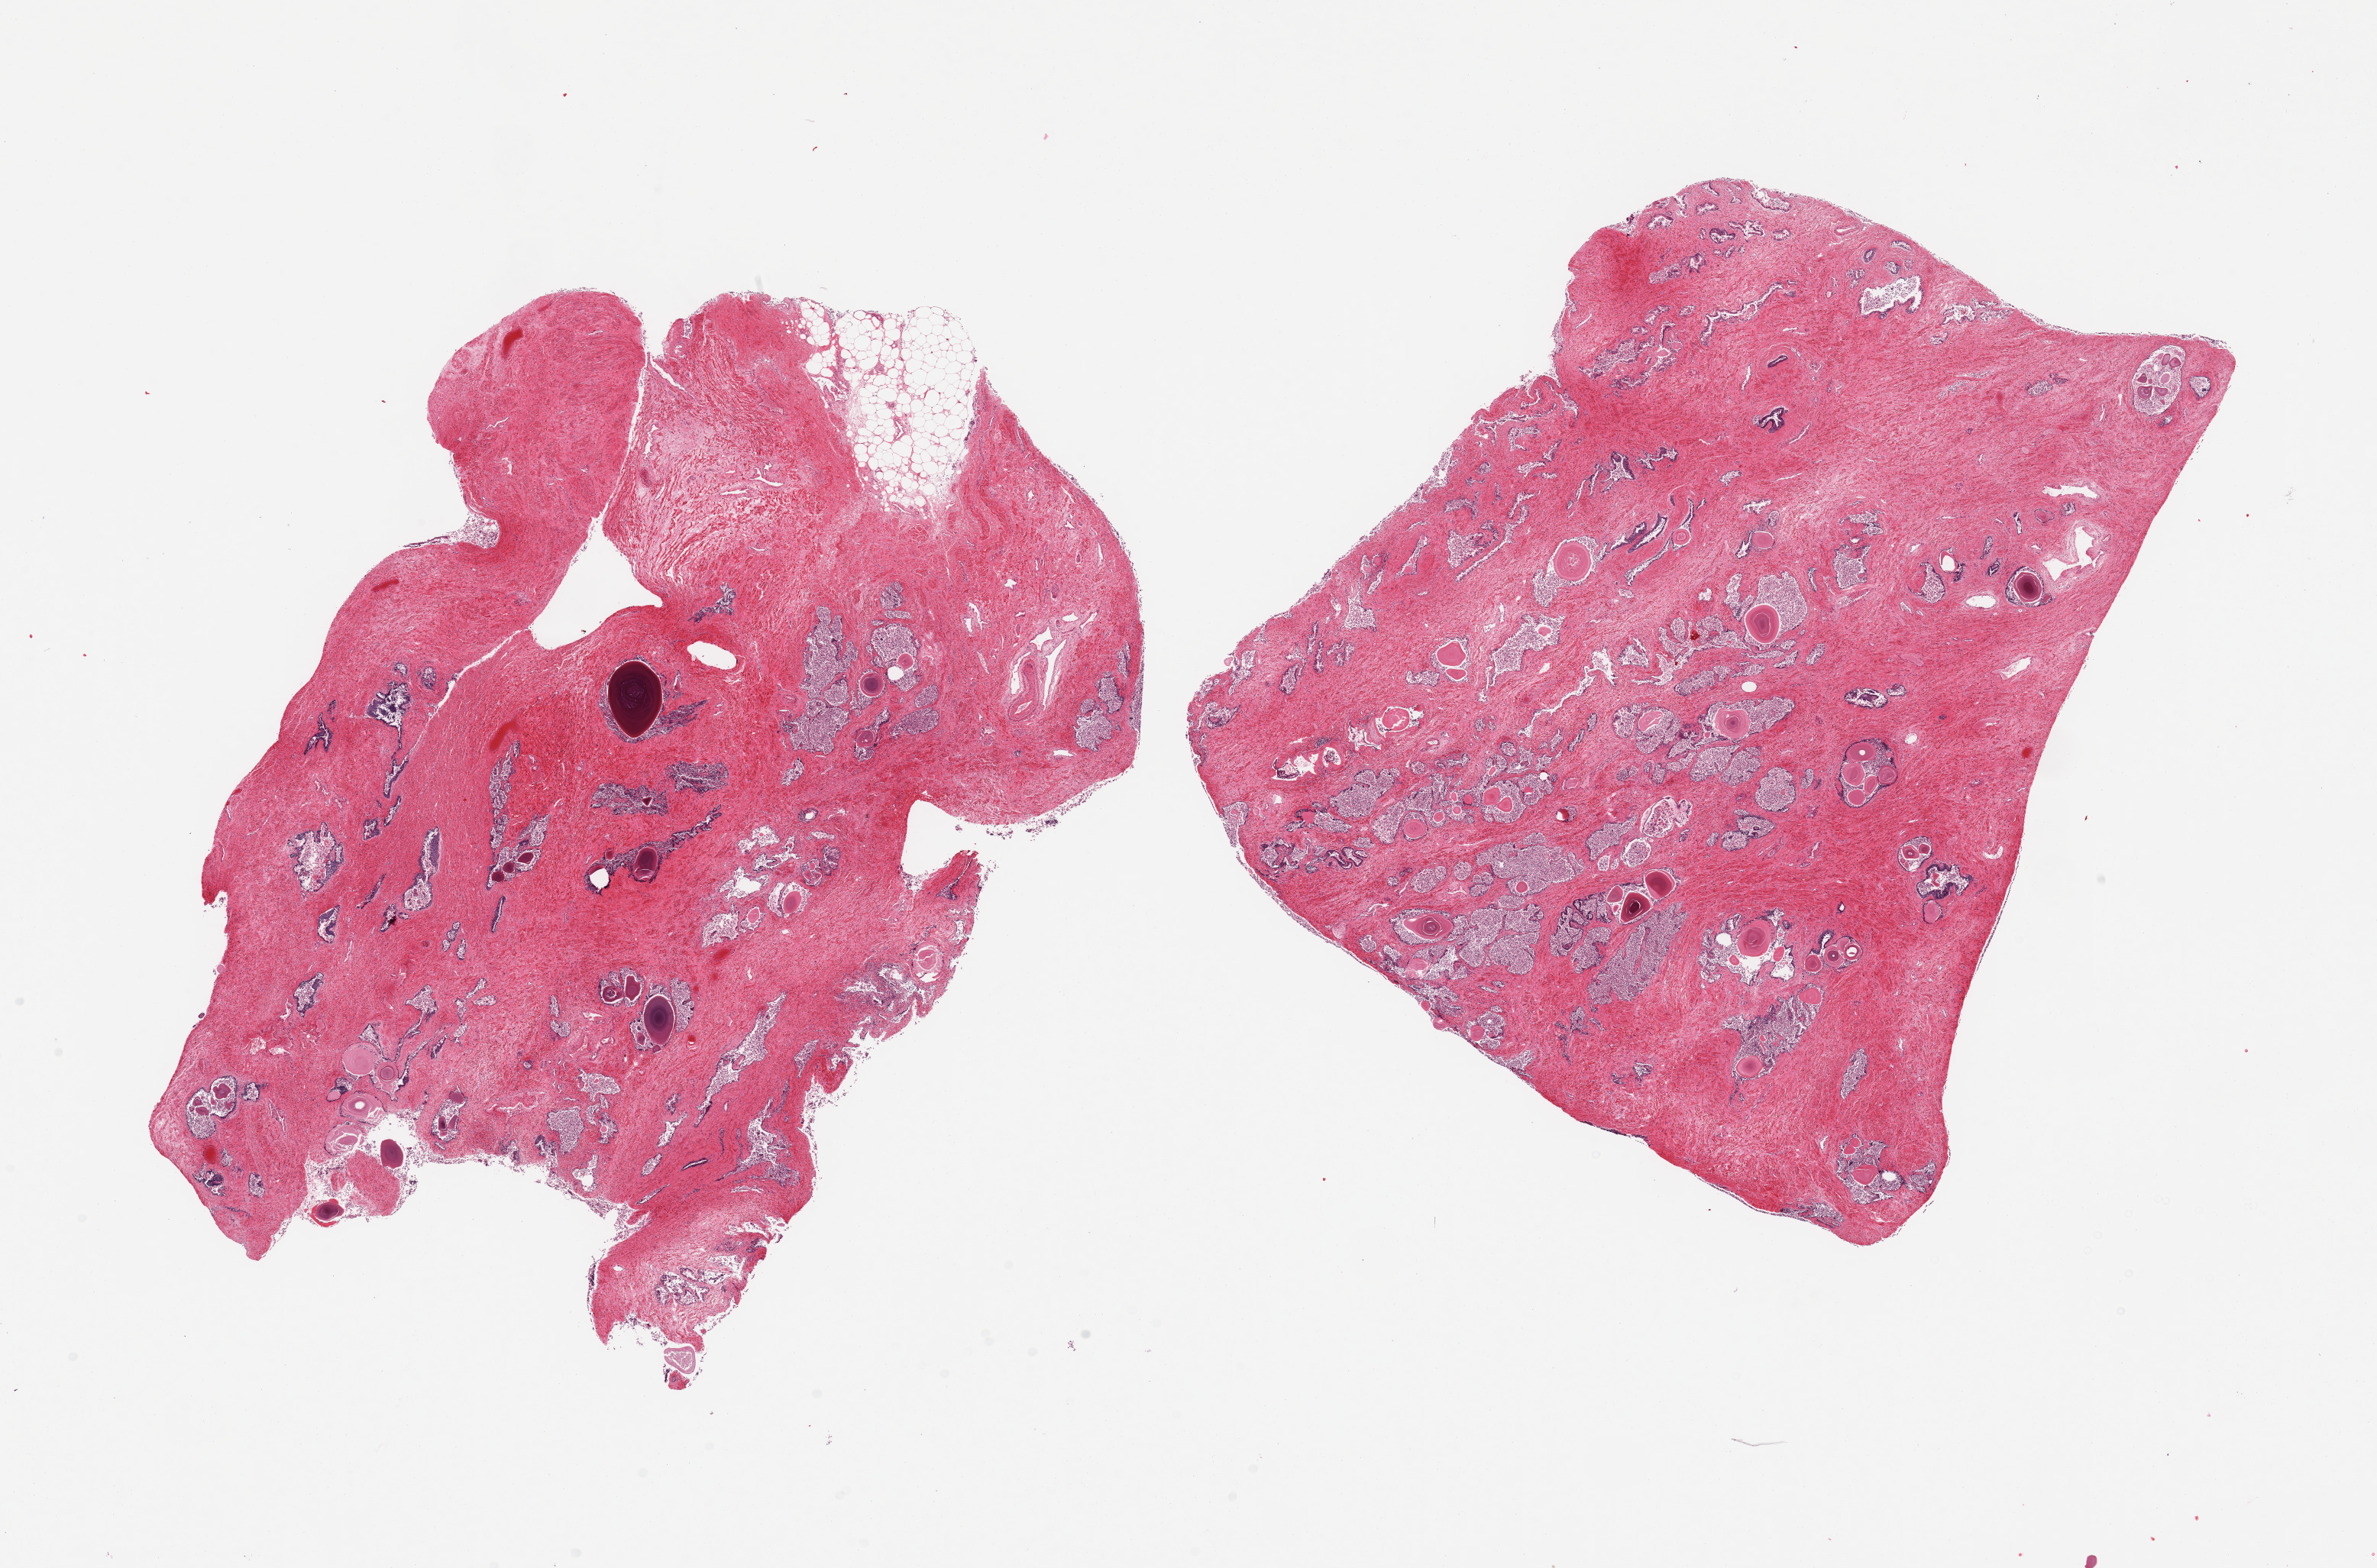
Digitized hematoxylin and eosin (H&E)-stained section — low-resolution overview of the scanned area, about 24.6 x 16.2 mm (from a 20x scan). PAXgene-fixed, paraffin-embedded tissue. Target tissue: prostate. Donor tissue sample. Donor: male.
Reviewer comment on this tissue sample: 2 pieces, glandular hyperplastic pattern.